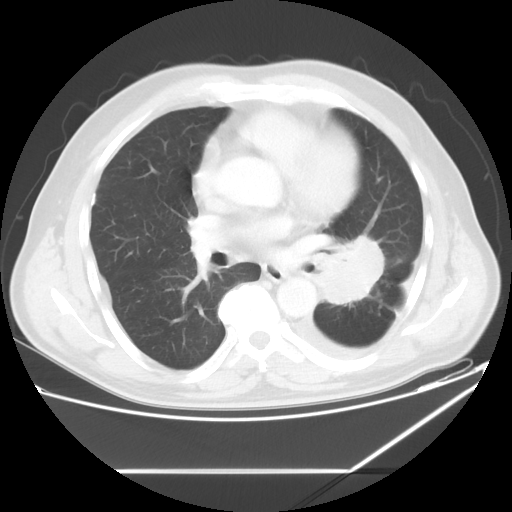
Chest CT, one axial slice; position 31 of 60 along the scan axis; lung window (W 1500 / L -600 HU); 5 mm slice thickness; 512 × 512 image matrix, field of view 395 × 395 mm. Patient: male, 62 years. From the clinical record (not read from this slice): clinical TNM (as recorded): T3 N0 M1.
Outlined on this slice (rectangle marked by the reading radiologist):
- lung tumour (recorded histology: adenocarcinoma): bounding box <317,235,387,309> (left, top, right, bottom; pixels)
- lung tumour (recorded histology: adenocarcinoma): <318,230,389,308>